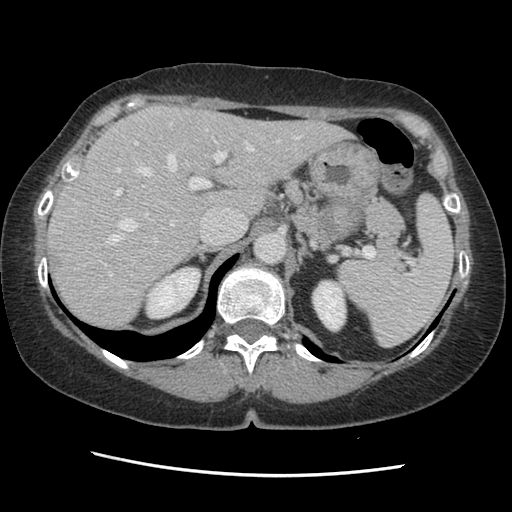
Contrast-enhanced abdominal CT, one axial slice; soft-tissue window (W 400 / L 40 HU); 2.5 mm slice thickness; 512 × 512 image matrix. Female patient, age 61 years. Case-level facts recorded for this patient, not image findings: diagnosis: colorectal cancer liver metastases, imaged before liver resection; multiple liver metastases: no; largest metastasis: 2.4 cm; chemotherapy before resection: no.
Outlined on this slice (expert manual segmentation):
- hepatic veins: bounding box <110,122,301,244> (left, top, right, bottom; pixels)
- liver: <49,107,347,330>
- planned liver remnant (the part of the liver to remain after resection): <49,107,346,330>
- portal vein (with intrahepatic branches): <104,141,227,276>